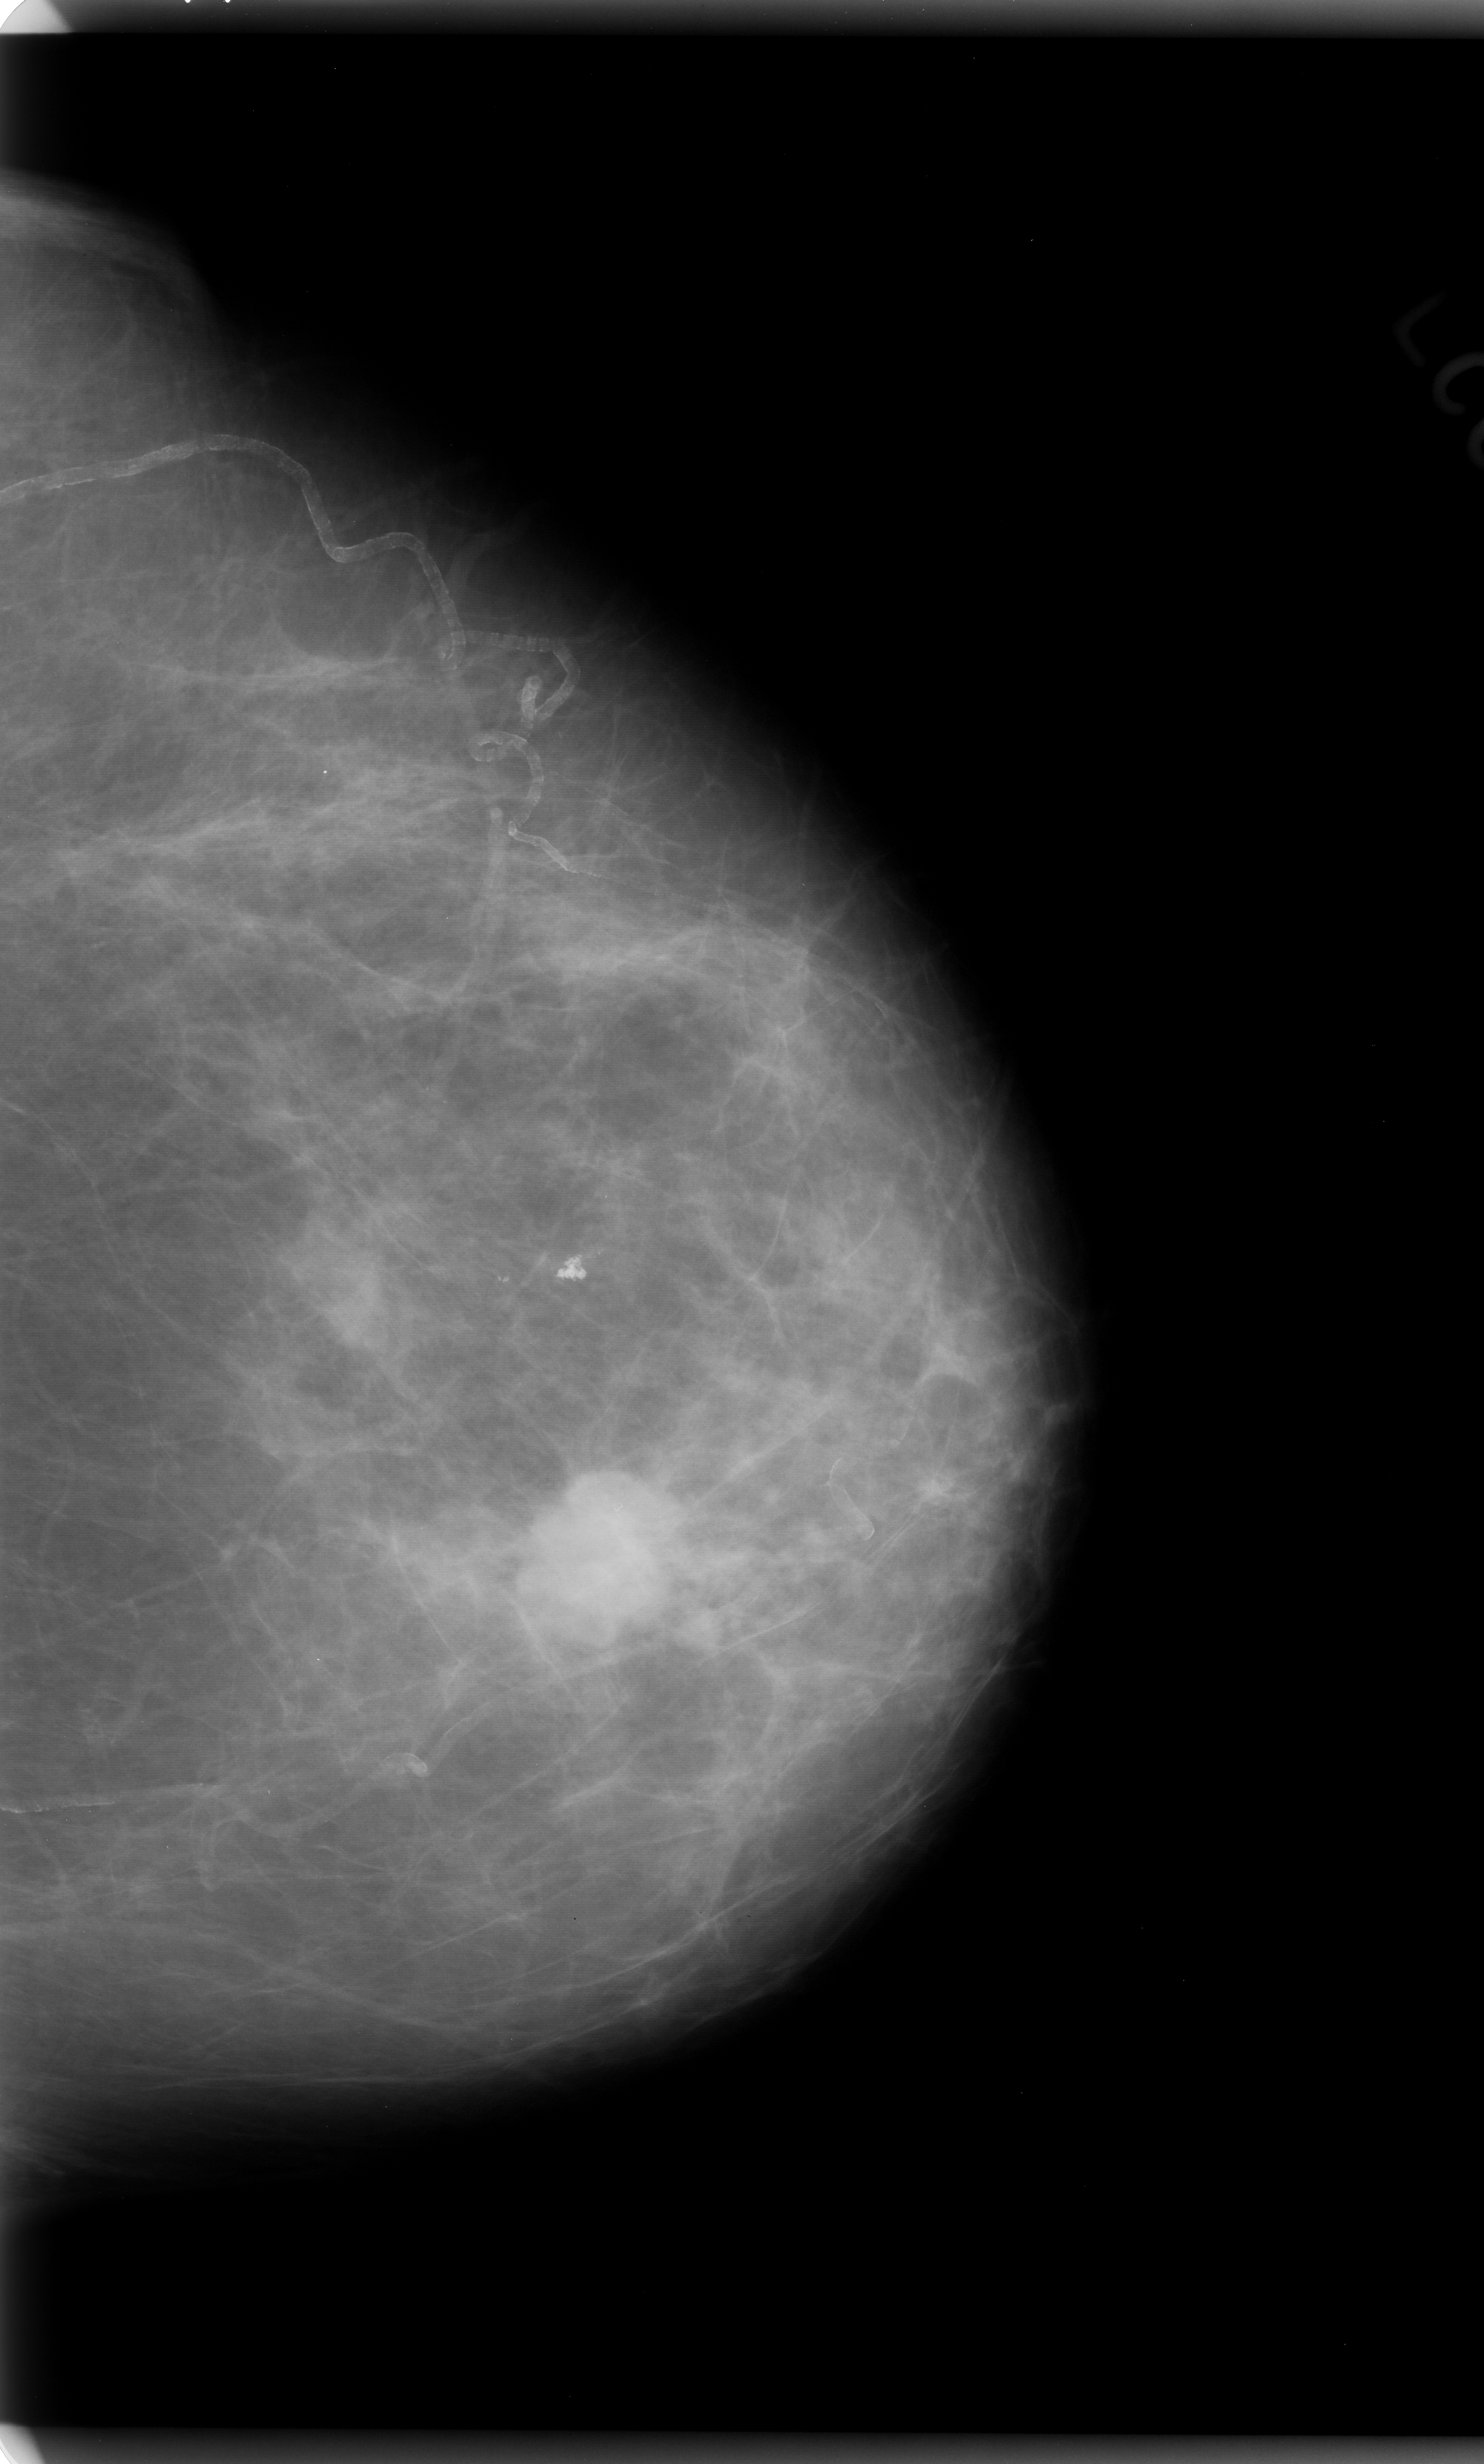
Scanned film-screen mammogram; left breast; CC view; 1484 × 2464 image matrix.
Expert-marked regions of interest on this image (one box per marked abnormality):
- mass, shape lobulated, margins microlobulated; BI-RADS assessment category 5; subtlety rating 5 on a 1 (subtle) to 5 (obvious) scale; pathology result (as recorded, not read from the image): malignant: bounding box <515,1486,672,1673> (left, top, right, bottom; pixels)